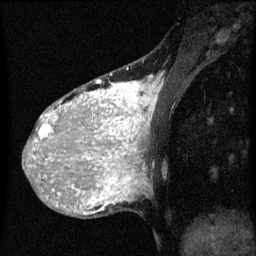
Breast MRI (dynamic contrast-enhanced), one sagittal slice. Position 17 of 60 along the scan axis. Dynamic contrast-enhanced series, image 2 of 3 at this slice position (ordered by acquisition). 1.5 T. TE 4.2 ms, TR 8 ms. 2 mm slice thickness. 256 × 256 image matrix, field of view 180 × 180 mm. Female patient, age 36 years.
Annotated regions visible in this slice (semi-automatically segmented with operator editing):
- analysis volume of interest (the breast-tissue region the enhancement analysis was run in; not a lesion): bounding box [x1, y1, x2, y2] px = [32, 68, 161, 161]
- tumour enhancement mask (voxels above the 70 % enhancement threshold inside the analysis volume of interest): [32, 82, 159, 161]